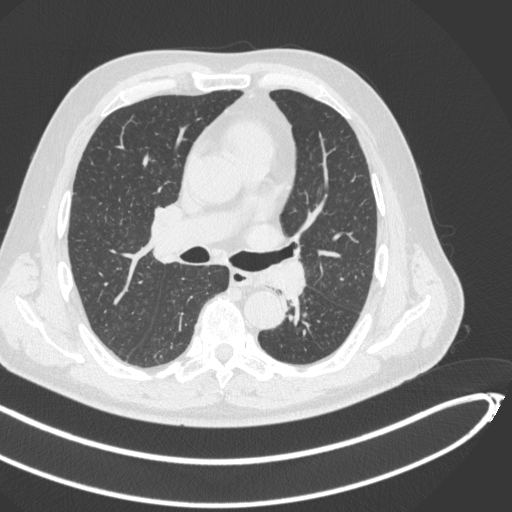
Chest CT, one axial slice; position 270 of 466 along the scan axis; lung window (W 1500 / L -600 HU); 1 mm slice thickness; 512 × 512 image matrix. Patient: male, 64 years. Case-level facts recorded for this patient, not image findings: clinical TNM (as recorded): T1c N0 M0.
Structures marked on this image (rectangle marked by the reading radiologist):
- lung tumour (recorded histology: squamous cell carcinoma): bounding box (x1, y1, x2, y2) in pixels: (258, 257, 313, 300)